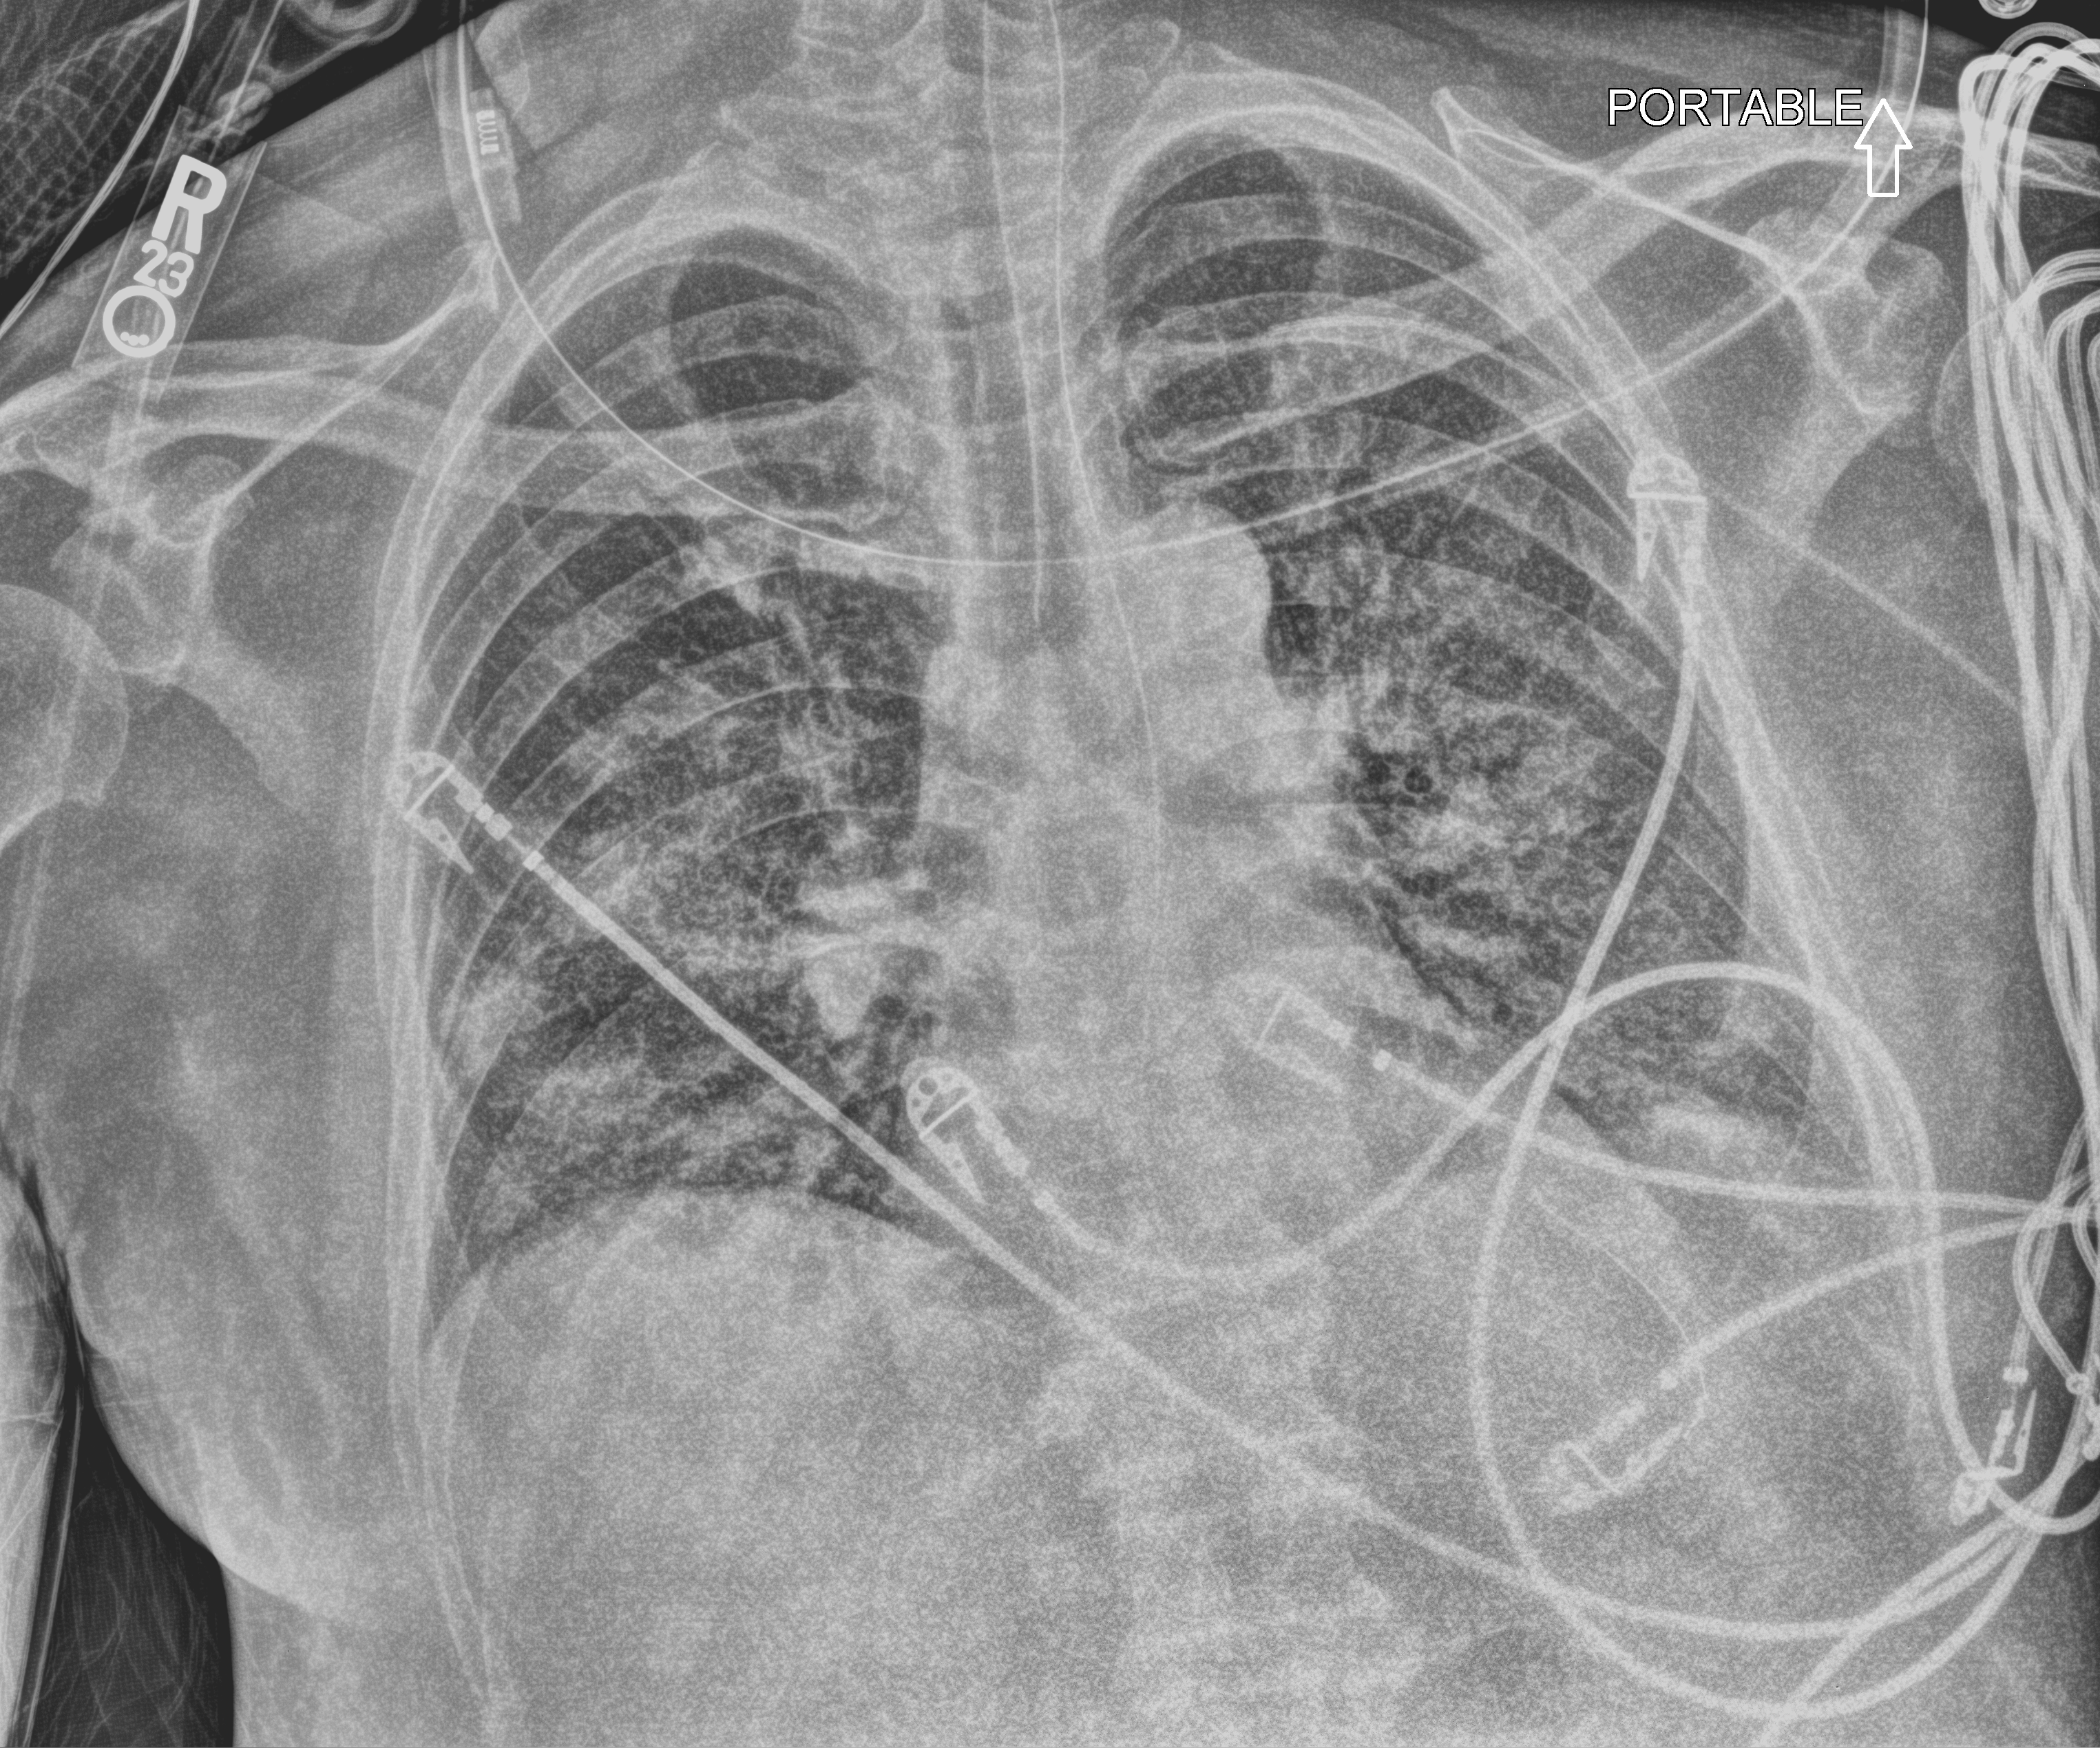
Chest X-ray (portable), anteroposterior (AP) projection. Patient hospitalised with COVID-19; male, aged 60–74 years.
Admission-level facts for this patient (not findings on this image; timing relative to this image not recorded): diabetes (admission record): yes; length of hospital stay: 14 days.